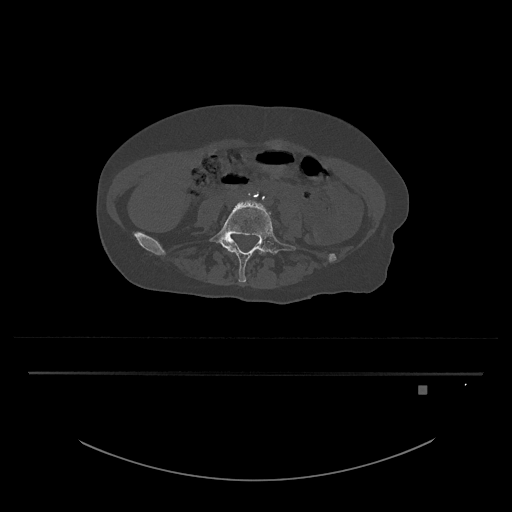
CT including the spine, one axial slice; slice 310 of 797 in the series (ordered by position); reconstruction kernel Br40s/3; 120 kVp; bone window (W 1800 / L 400 HU); 512 × 512 image matrix, field of view 500 × 500 mm. Patient: female, 57 years. Case-level facts recorded for this patient, not image findings: primary cancer: cervical.
Structures marked on this image (semi-automatically segmented with operator editing):
- L4 vertebra: bounding box <258,251,262,255> (left, top, right, bottom; pixels)